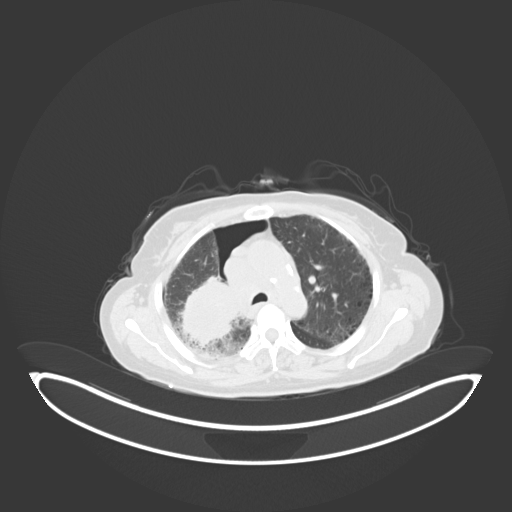
Chest CT, one axial slice. 120 kVp. Lung window (W 1500 / L -600 HU). 3 mm slice thickness. 512 × 512 image matrix, field of view 500 × 500 mm. Patient: female, 64 years. Case-level facts recorded for this patient, not image findings: clinical TNM (as recorded): T3 N3 M0.
Structures marked on this image (rectangle marked by the reading radiologist):
- lung tumour (recorded histology: squamous cell carcinoma): bounding box (x1, y1, x2, y2) in pixels: (176, 271, 240, 354)